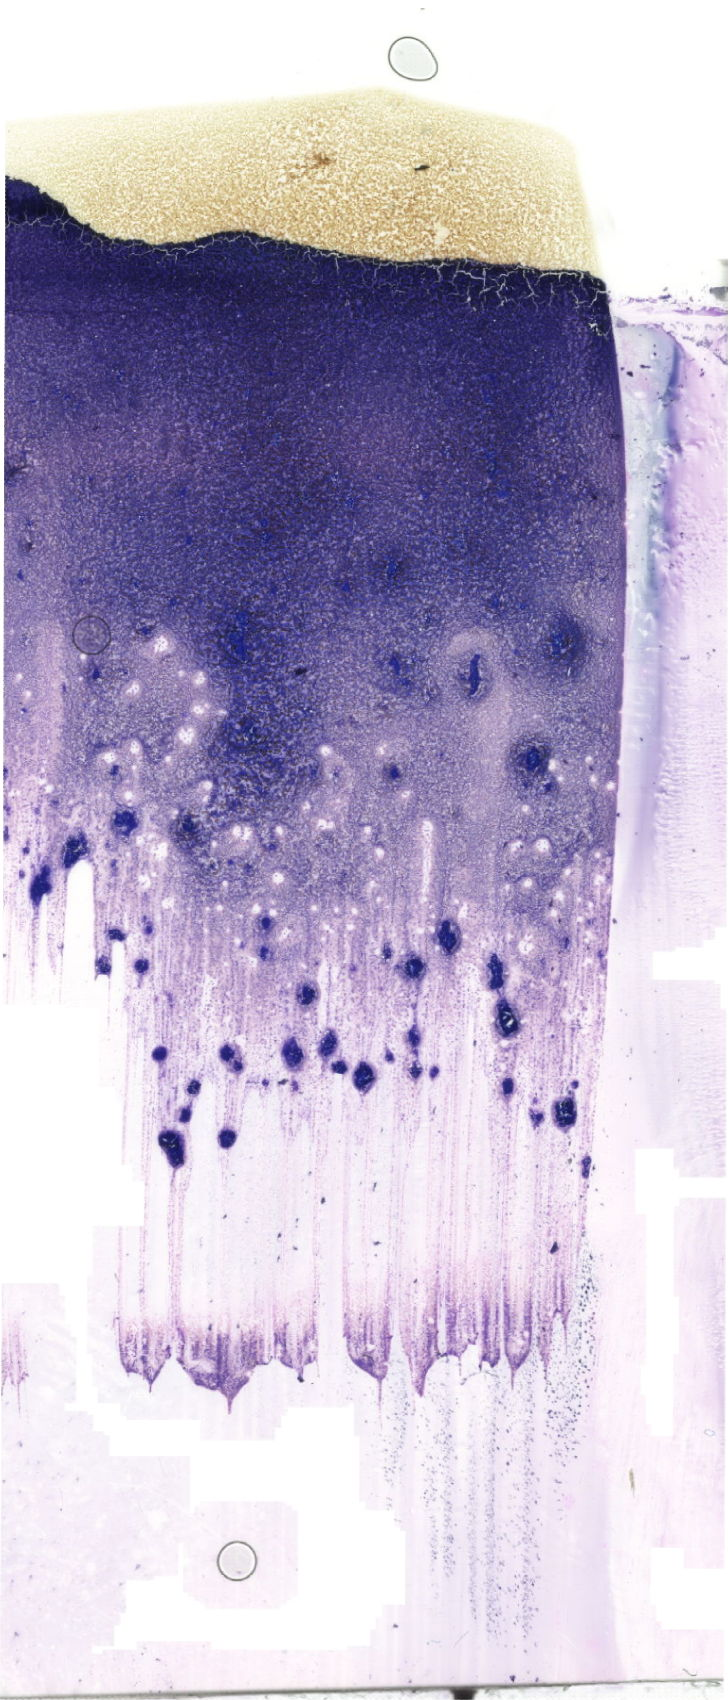
May-Grünwald-Giemsa (MGG)-stained marrow aspirate smear (whole slide), low-resolution overview of the scanned area, about 20.6 x 48.2 mm. Female patient.
* diagnosis: Acute Myeloid Leukemia with Maturation